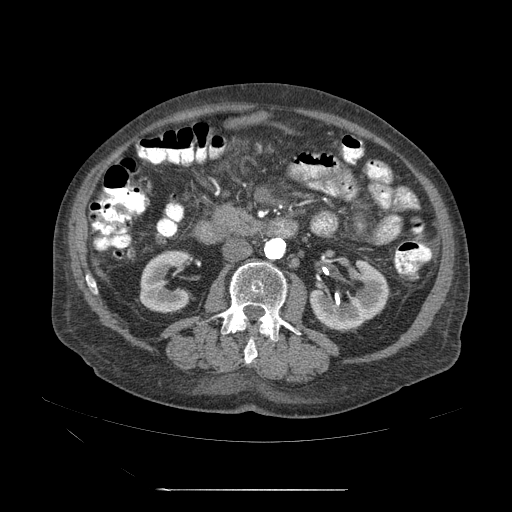
Contrast-enhanced abdominal CT (liver protocol), one axial slice; slice 2 of 71 in the series (ordered by position); reconstruction kernel STANDARD; 120 kVp; soft-tissue window (W 400 / L 40 HU); 512 × 512 image matrix, field of view 440 × 440 mm. Case-level facts recorded for this patient, not image findings: diagnosis: hepatocellular carcinoma (patient treated with transarterial chemoembolisation; whether this scan precedes or follows treatment is not stated here); TNM stage (as recorded): Stage-II; Child-Pugh class: A; tumour nodularity: multinodular; tumour size: 1 cm.
Annotated regions visible in this slice (semi-automatic segmentation, software-assisted and operator-edited):
- abdominal aorta: bounding box (x1, y1, x2, y2) in pixels: (265, 238, 286, 261)